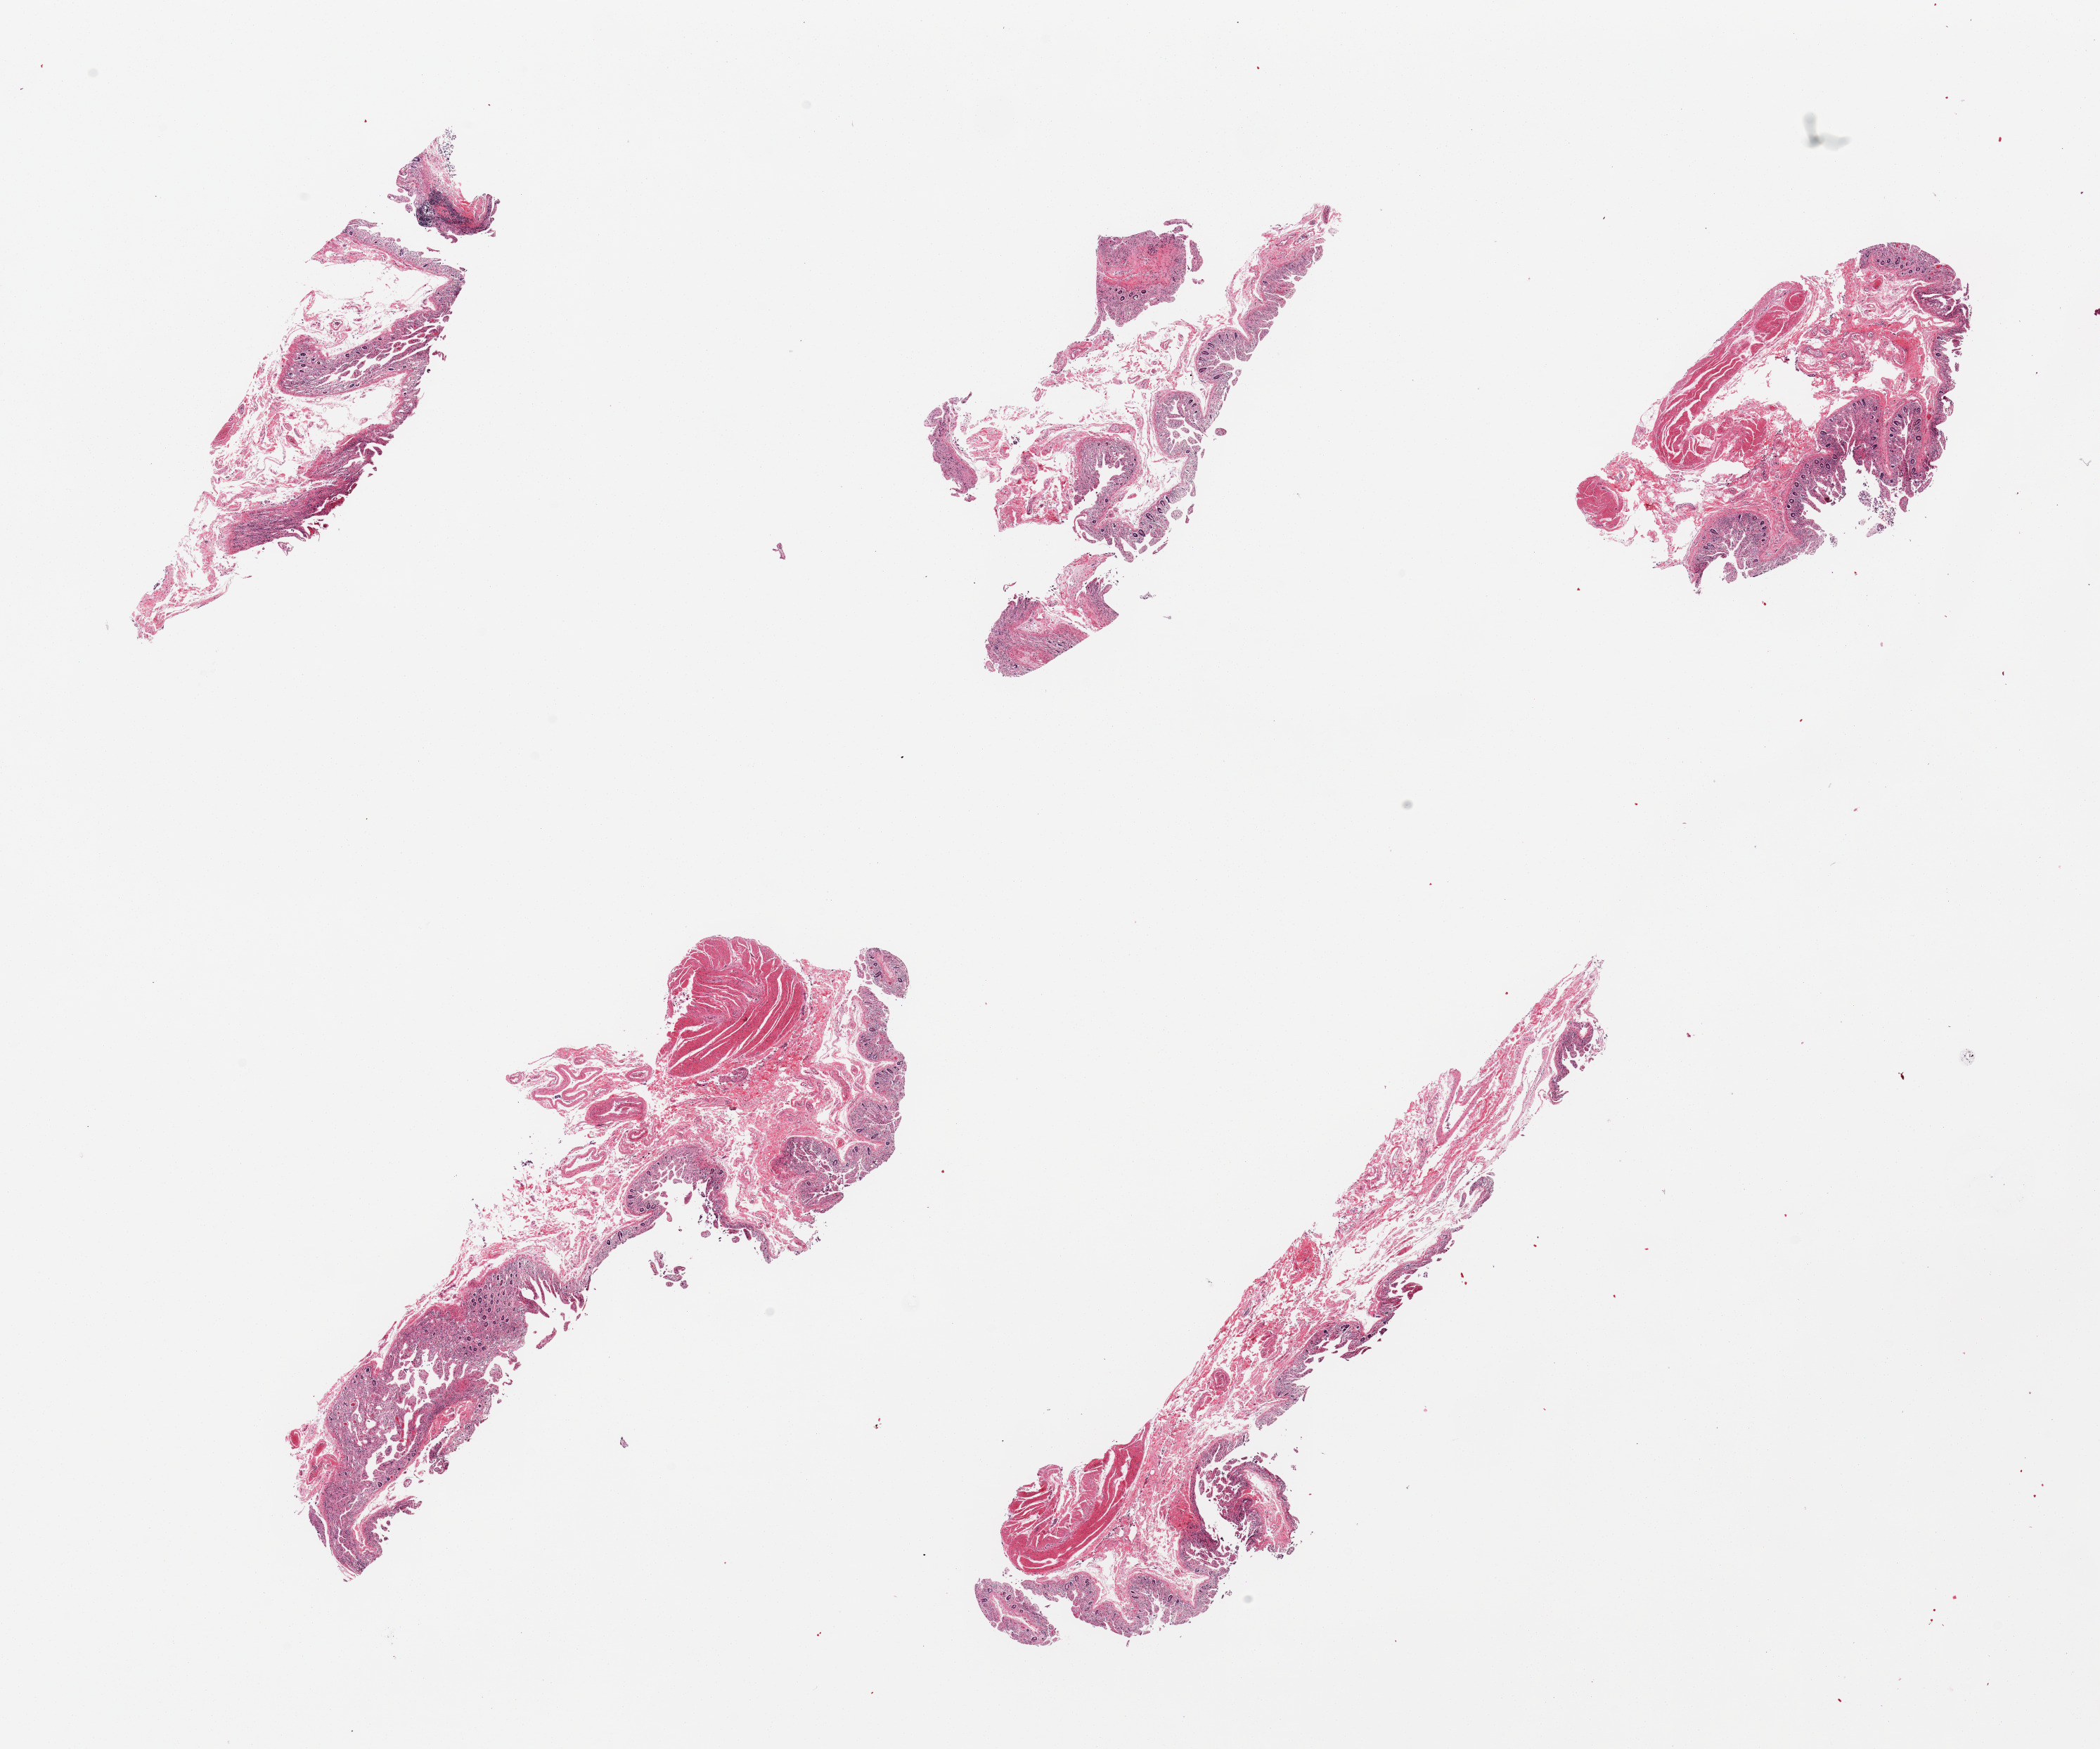
Digitized hematoxylin and eosin (H&E)-stained section, whole scanned area (about 23.6 x 19.7 mm) shown as a low-resolution overview. PAXgene-fixed, paraffin-embedded tissue. Section of ileum (target tissue). Tissue donor sample. Donor sex: female.
- review note (as recorded): 5 pieces; moderatley to severely autolyzed mucosa with muscularis (not target), no significant lymphoid component (target)